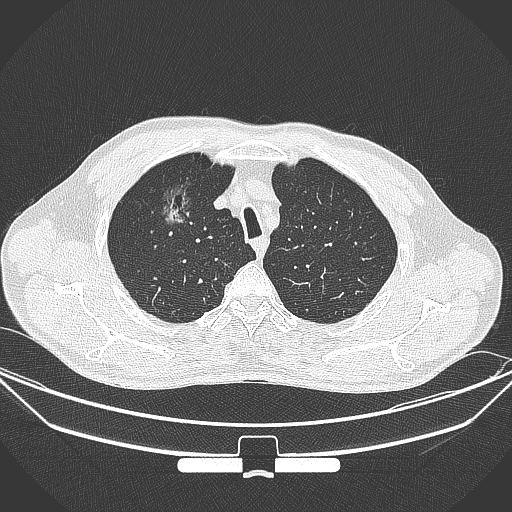
Chest CT, one axial slice; slice 284 of 355 in the series (ordered by position); 120 kVp; lung window (W 1500 / L -600 HU); 1 mm slice thickness; 512 × 512 image matrix. Male patient, age 67 years. Case-level facts recorded for this patient, not image findings: clinical TNM (as recorded): T1c N0 M0; histopathological grade: G2.
Outlined on this slice (rectangle marked by the reading radiologist):
- lung tumour (recorded histology: adenocarcinoma): box from (x=153, y=171) to (x=198, y=232) px